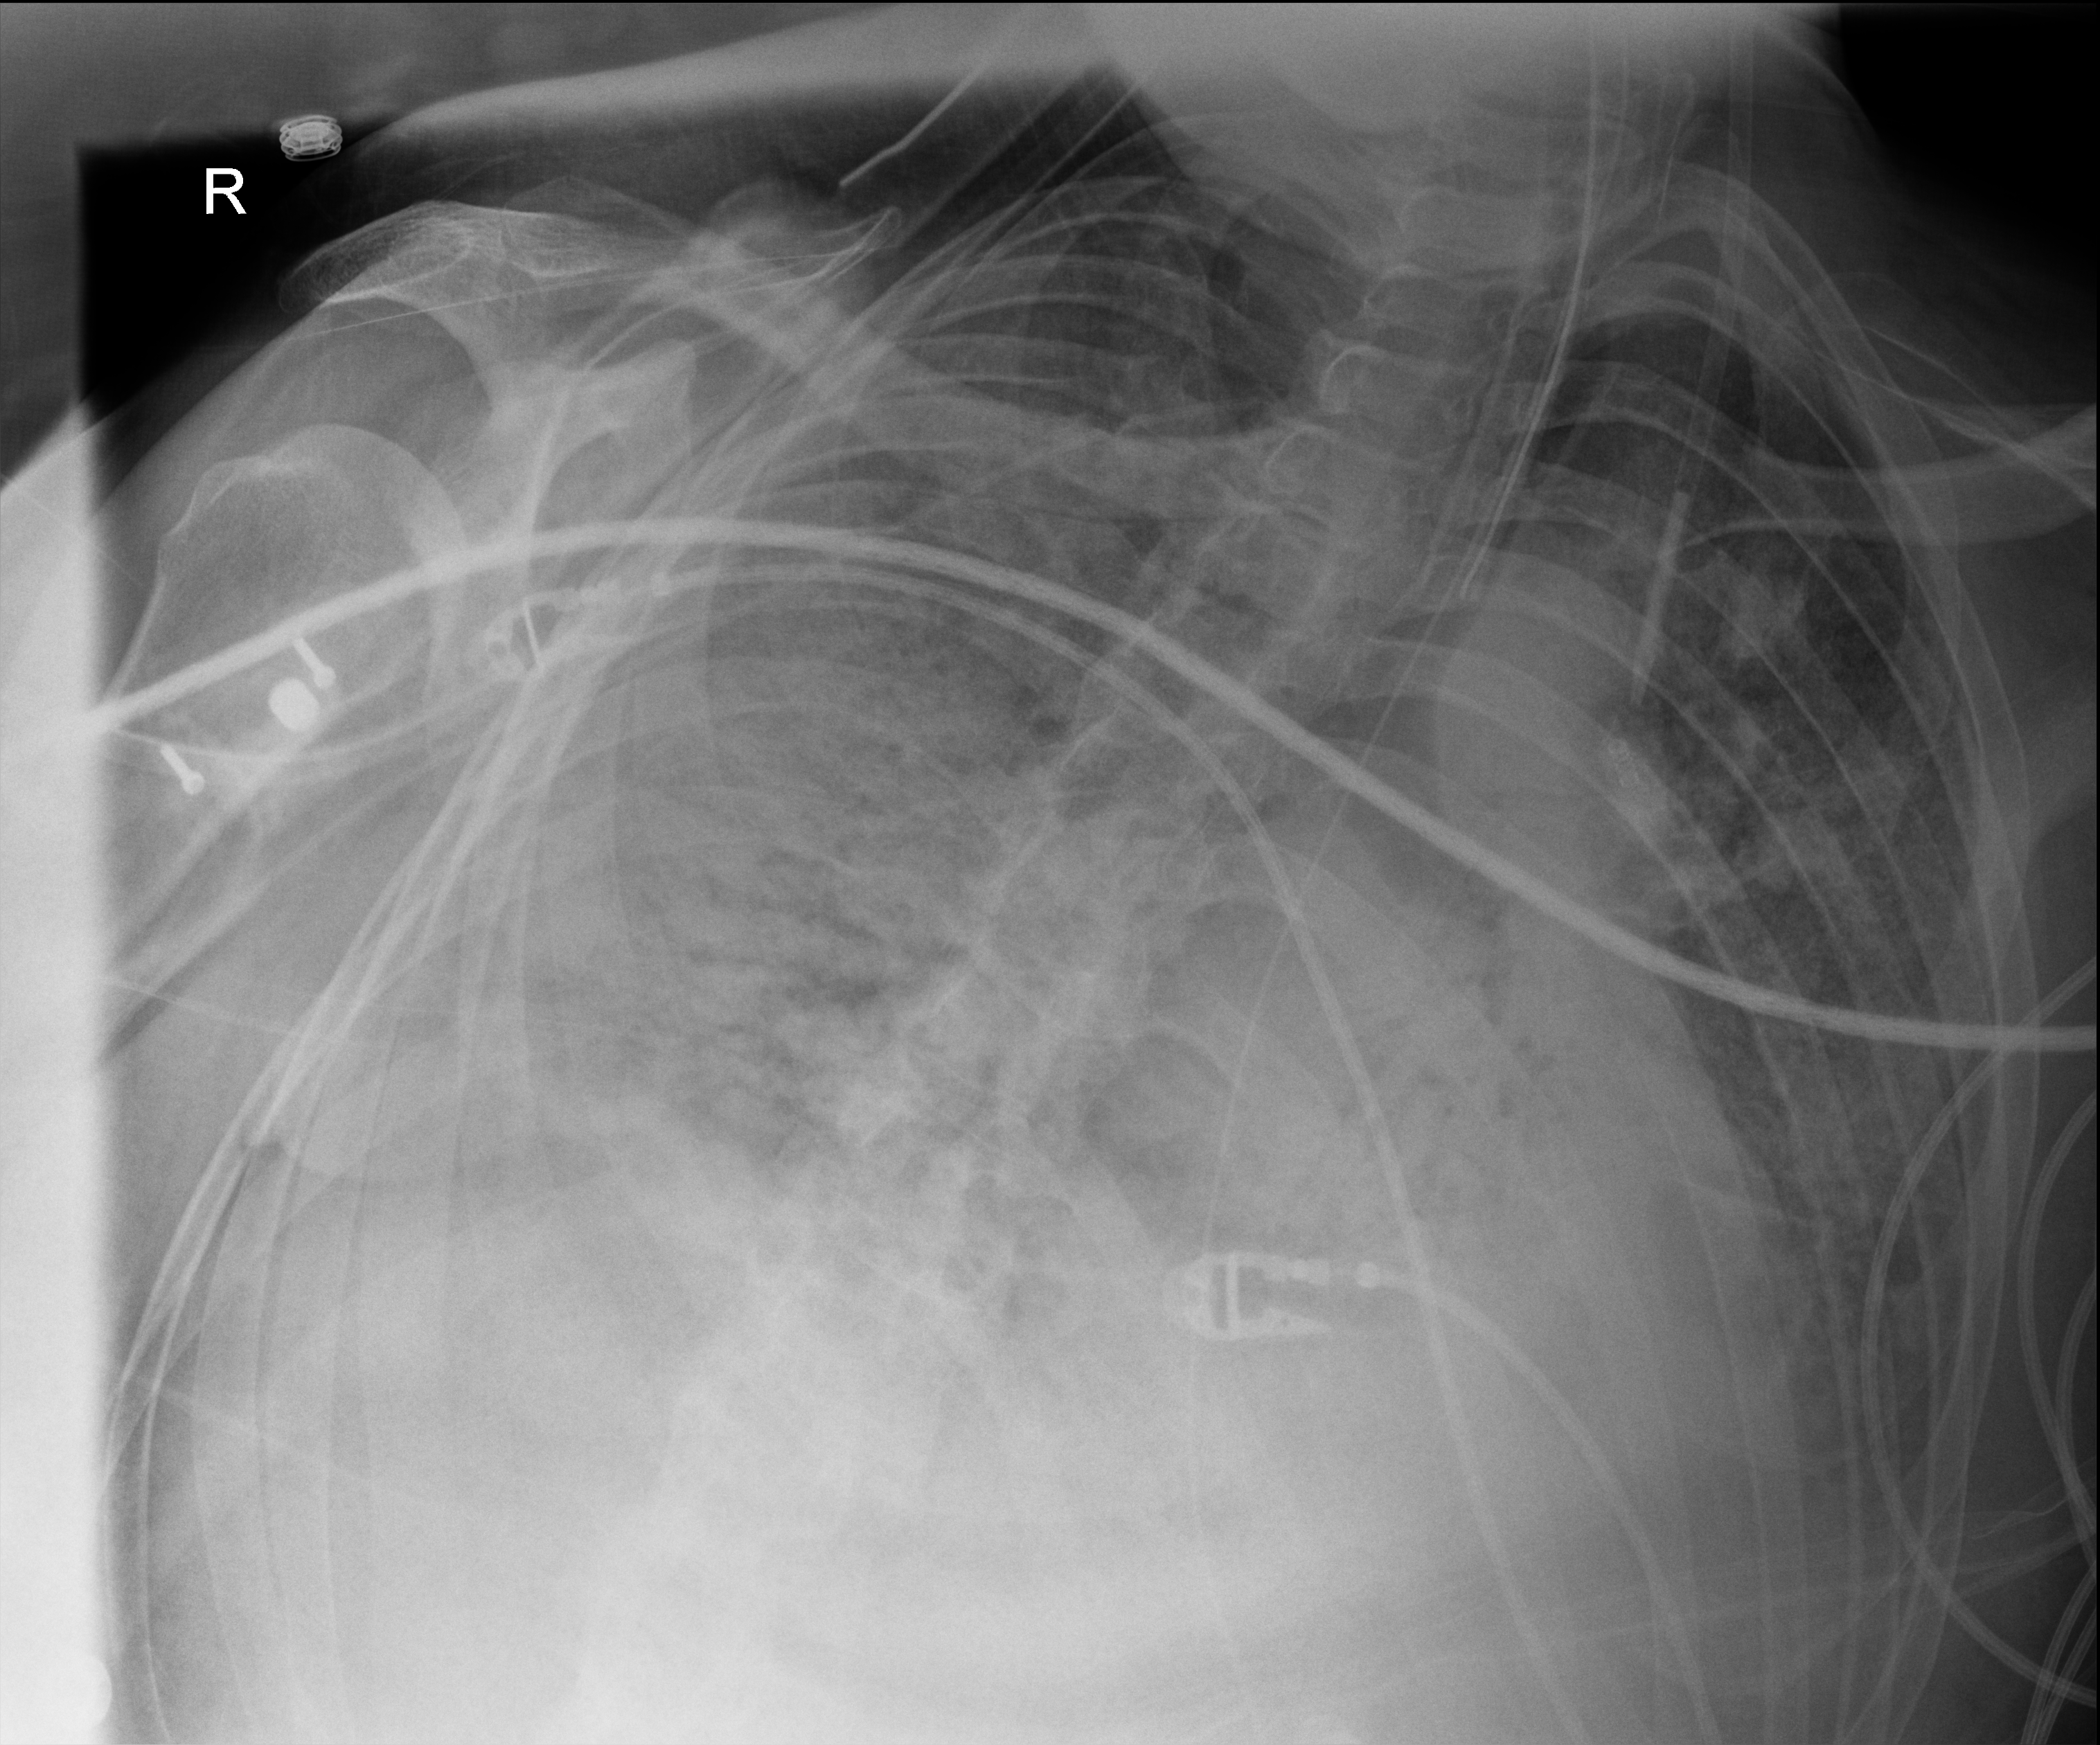
Portable chest radiograph, anteroposterior (AP) projection. Patient hospitalised with COVID-19; male, aged 18–59 years.
Hospital-stay facts (about this admission, not read from this image; timing relative to this image not recorded):
- chronic kidney disease (admission record): no
- mechanically ventilated during this hospital stay: yes